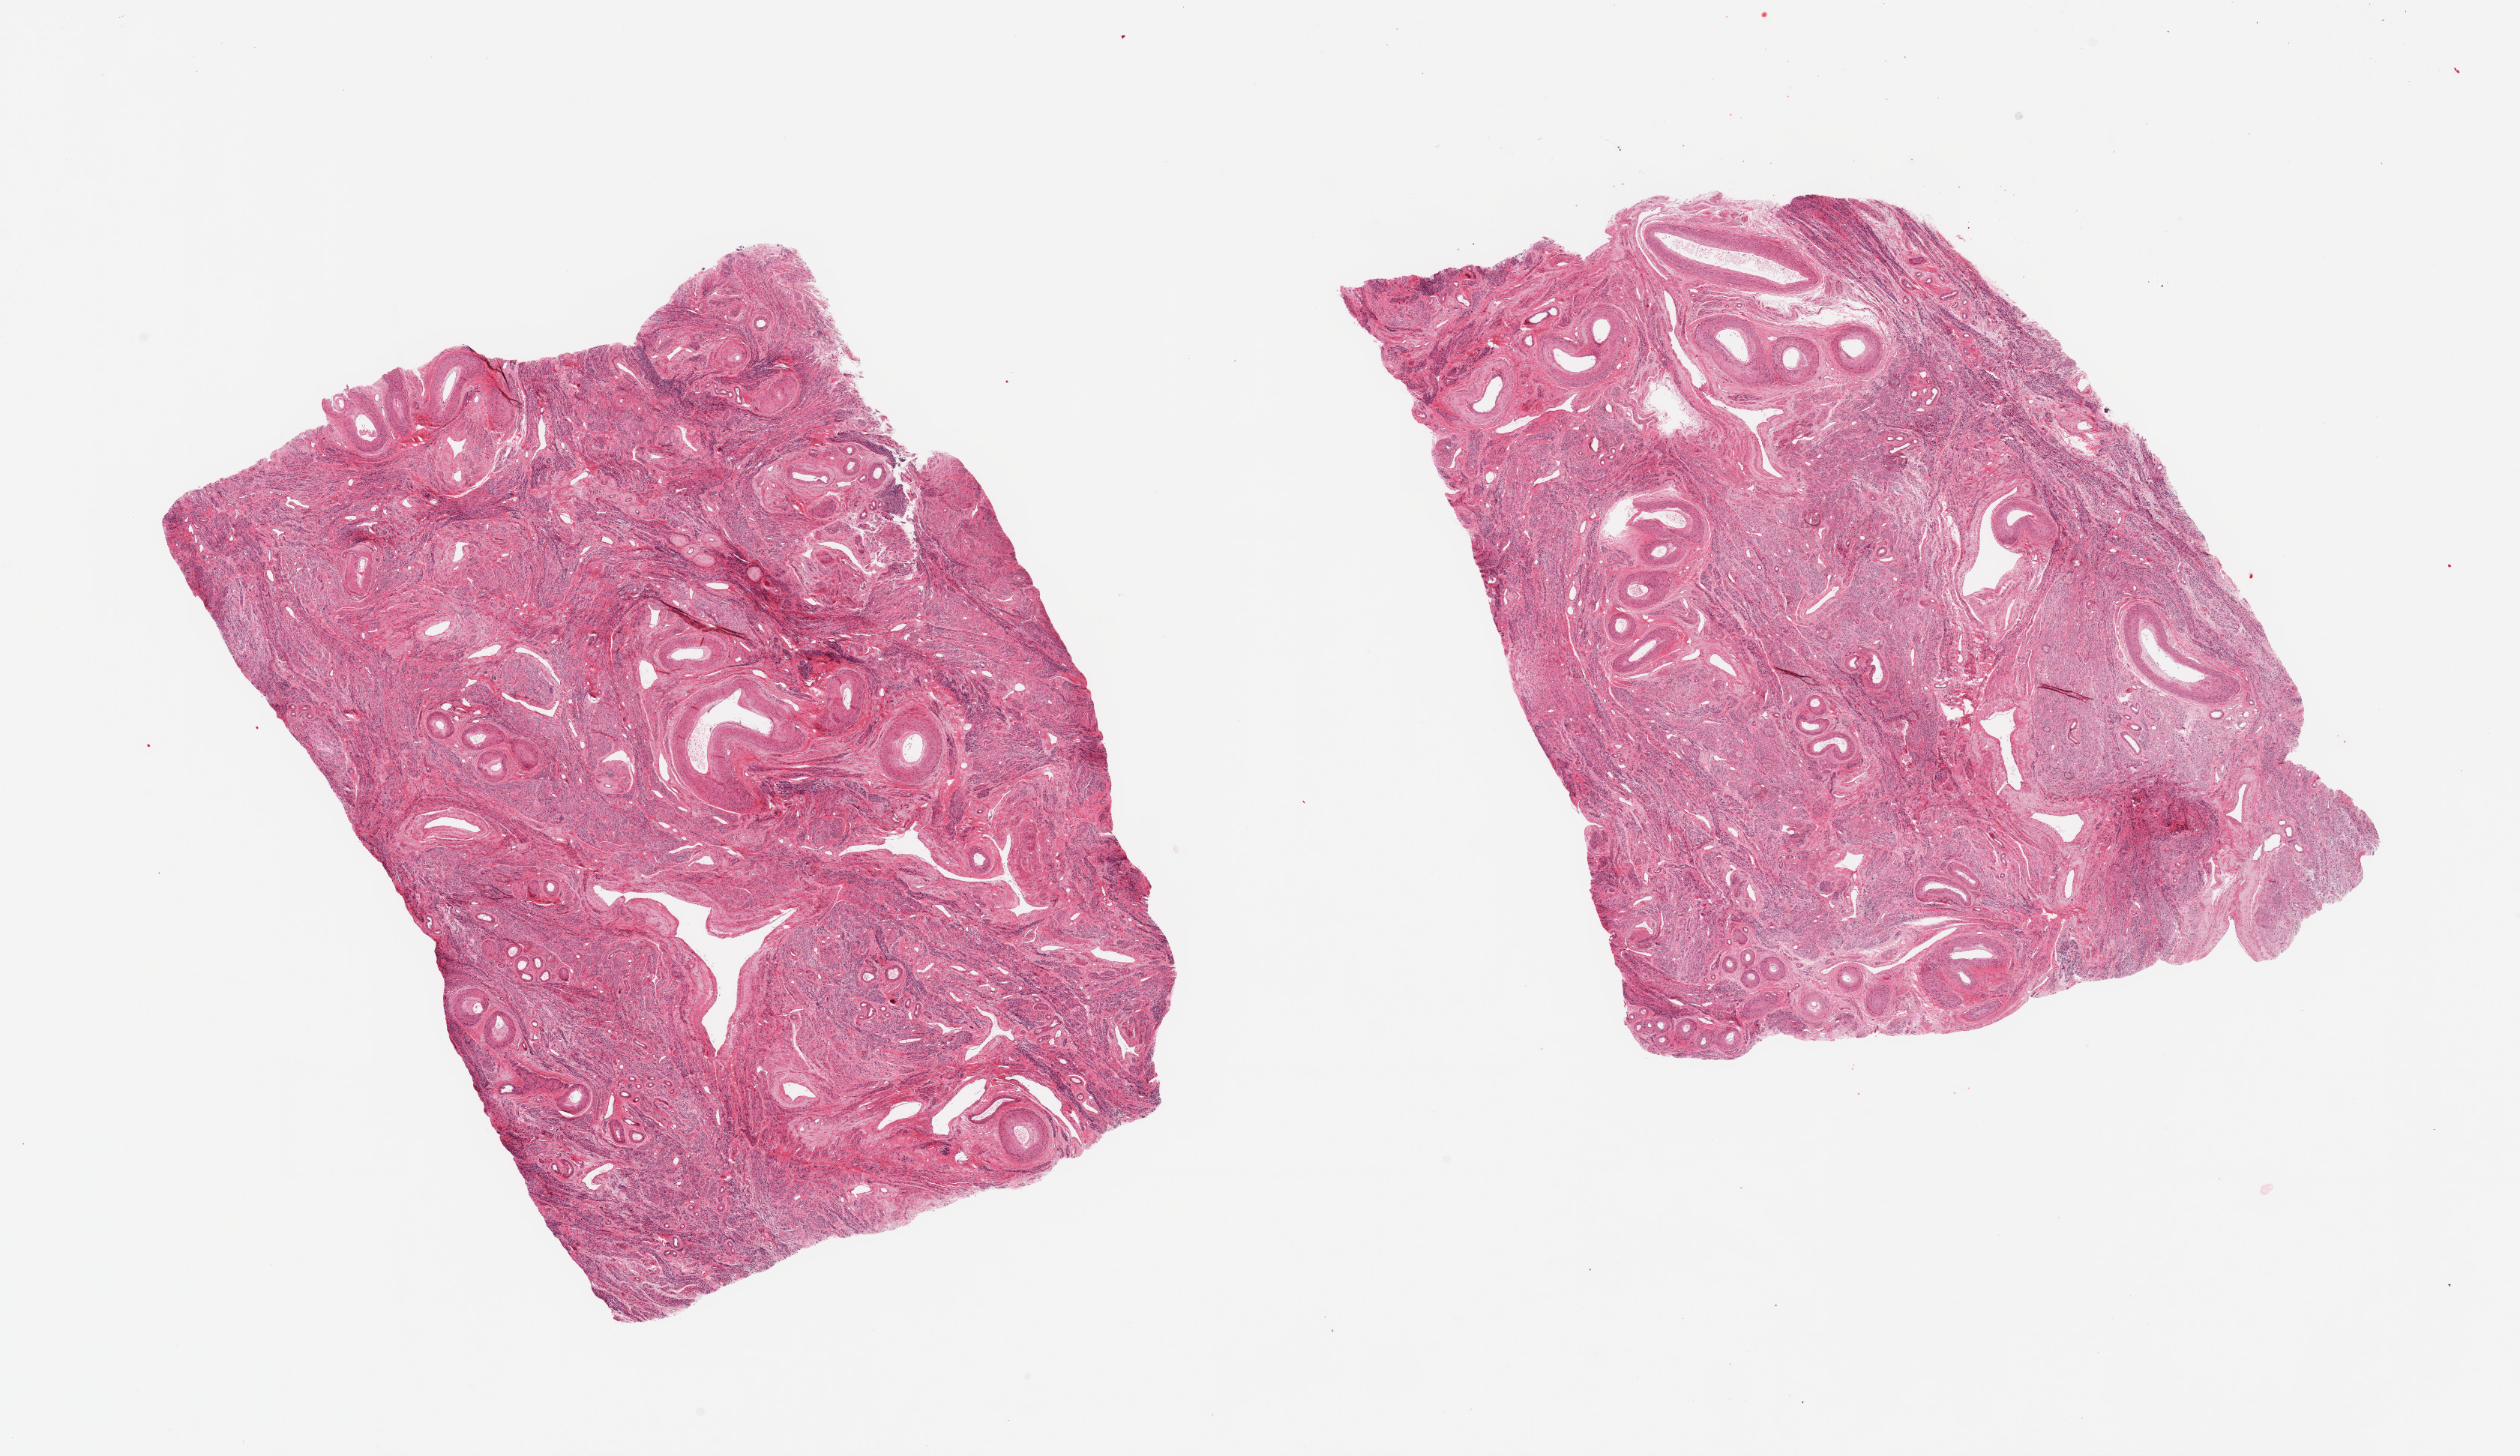
Whole-slide image, H&E stain, low-resolution overview of the scanned area, about 26.6 x 15.4 mm, PAXgene-fixed, paraffin-embedded tissue, sampled site (target tissue): uterus, donor tissue sample. Donor sex: female.
Review note (as recorded): 2 pieces; largely vascularized myometrium with no endometrium in these cuts.